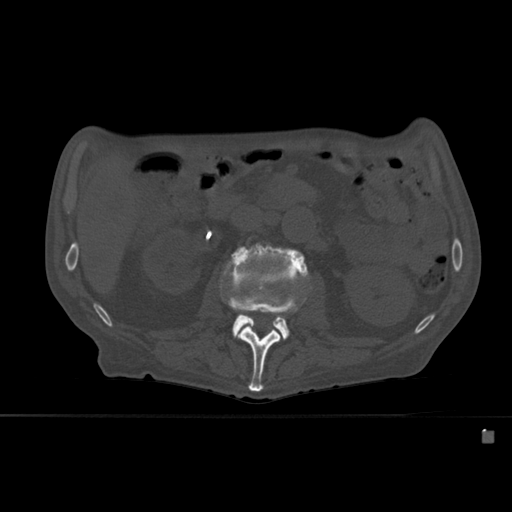
CT including the spine, one axial slice. Slice 226 of 527 in the series (ordered by position). Bone window (W 1800 / L 400 HU). 512 × 512 image matrix, field of view 373 × 373 mm. Patient: male, 78 years. Case-level facts recorded for this patient, not image findings: primary cancer: prostate.
Structures marked on this image (semi-automatic segmentation, software-assisted and operator-edited):
- L2 vertebra: bounding box <228,283,312,392> (left, top, right, bottom; pixels)
- L3 vertebra: <220,243,309,340>